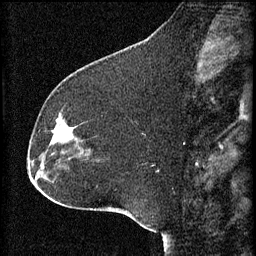
Breast MRI (dynamic contrast-enhanced), one sagittal slice; position 23 of 60 along the scan axis; 3 images stored at this slice position (order not interpretable as contrast timing); 1.5 T; TE 4.2 ms, TR 8.2 ms; 256 × 256 image matrix. Patient: female, 32 years.
Structures marked on this image (semi-automatically segmented with operator editing):
- analysis volume of interest (the breast-tissue region the enhancement analysis was run in; not a lesion): bounding box (x1, y1, x2, y2) in pixels: (47, 114, 84, 157)
- tumour enhancement mask (voxels above the 70 % enhancement threshold inside the analysis volume of interest): (52, 126, 65, 145)